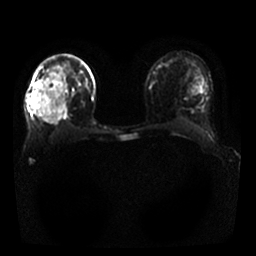
Breast MRI, one axial slice. Diffusion-weighted series; image 2 of 4 stored at this slice position (different b-values; order by instance number). 1.5 T. 4 mm slice thickness. 256 × 256 image matrix, field of view 330 × 330 mm. Female patient.
Structures marked on this image (expert manual segmentation):
- tumour on diffusion-weighted imaging: bounding box (x1, y1, x2, y2) in pixels: (29, 97, 37, 104)